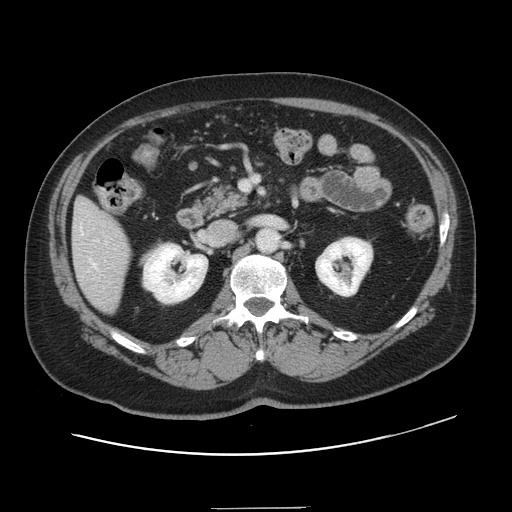
Contrast-enhanced abdominal CT, one axial slice; slice 61 of 143 in the series (ordered by position); intravenous contrast given; soft-tissue window (W 400 / L 40 HU); 512 × 512 image matrix, field of view 402 × 402 mm. Male patient, age 62 years. From the clinical record (not read from this slice): diagnosis: colorectal cancer liver metastases, imaged before liver resection; multiple liver metastases: yes; largest metastasis: 2.7 cm; disease in both lobes: no.
Outlined on this slice (manually delineated by an expert):
- hepatic veins: bounding box [x1, y1, x2, y2] px = [81, 228, 97, 268]
- liver: [73, 199, 131, 313]
- planned liver remnant (the part of the liver to remain after resection): [80, 200, 87, 205]
- portal vein (with intrahepatic branches): [96, 240, 107, 262]